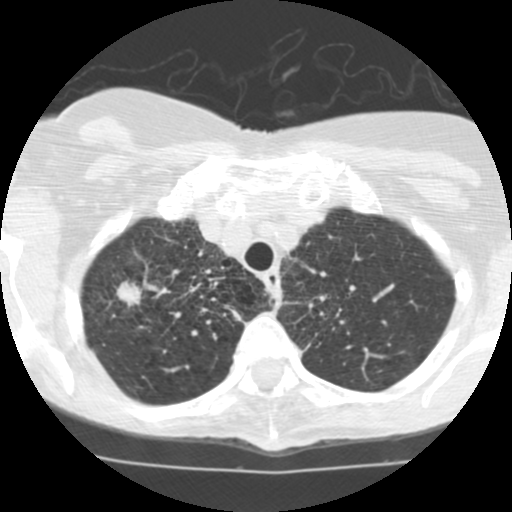
Low-dose screening chest CT, one axial slice. Position 95 of 115 along the scan axis. Reconstruction kernel STANDARD. Lung window (W 1500 / L -600 HU). 2.5 mm slice thickness. 512 × 512 image matrix.
Outlined on this slice (outlined manually by an expert reader):
- lesion 1 (tumor, upper lobe of right lung): bounding box (x1, y1, x2, y2) in pixels: (117, 281, 142, 306)